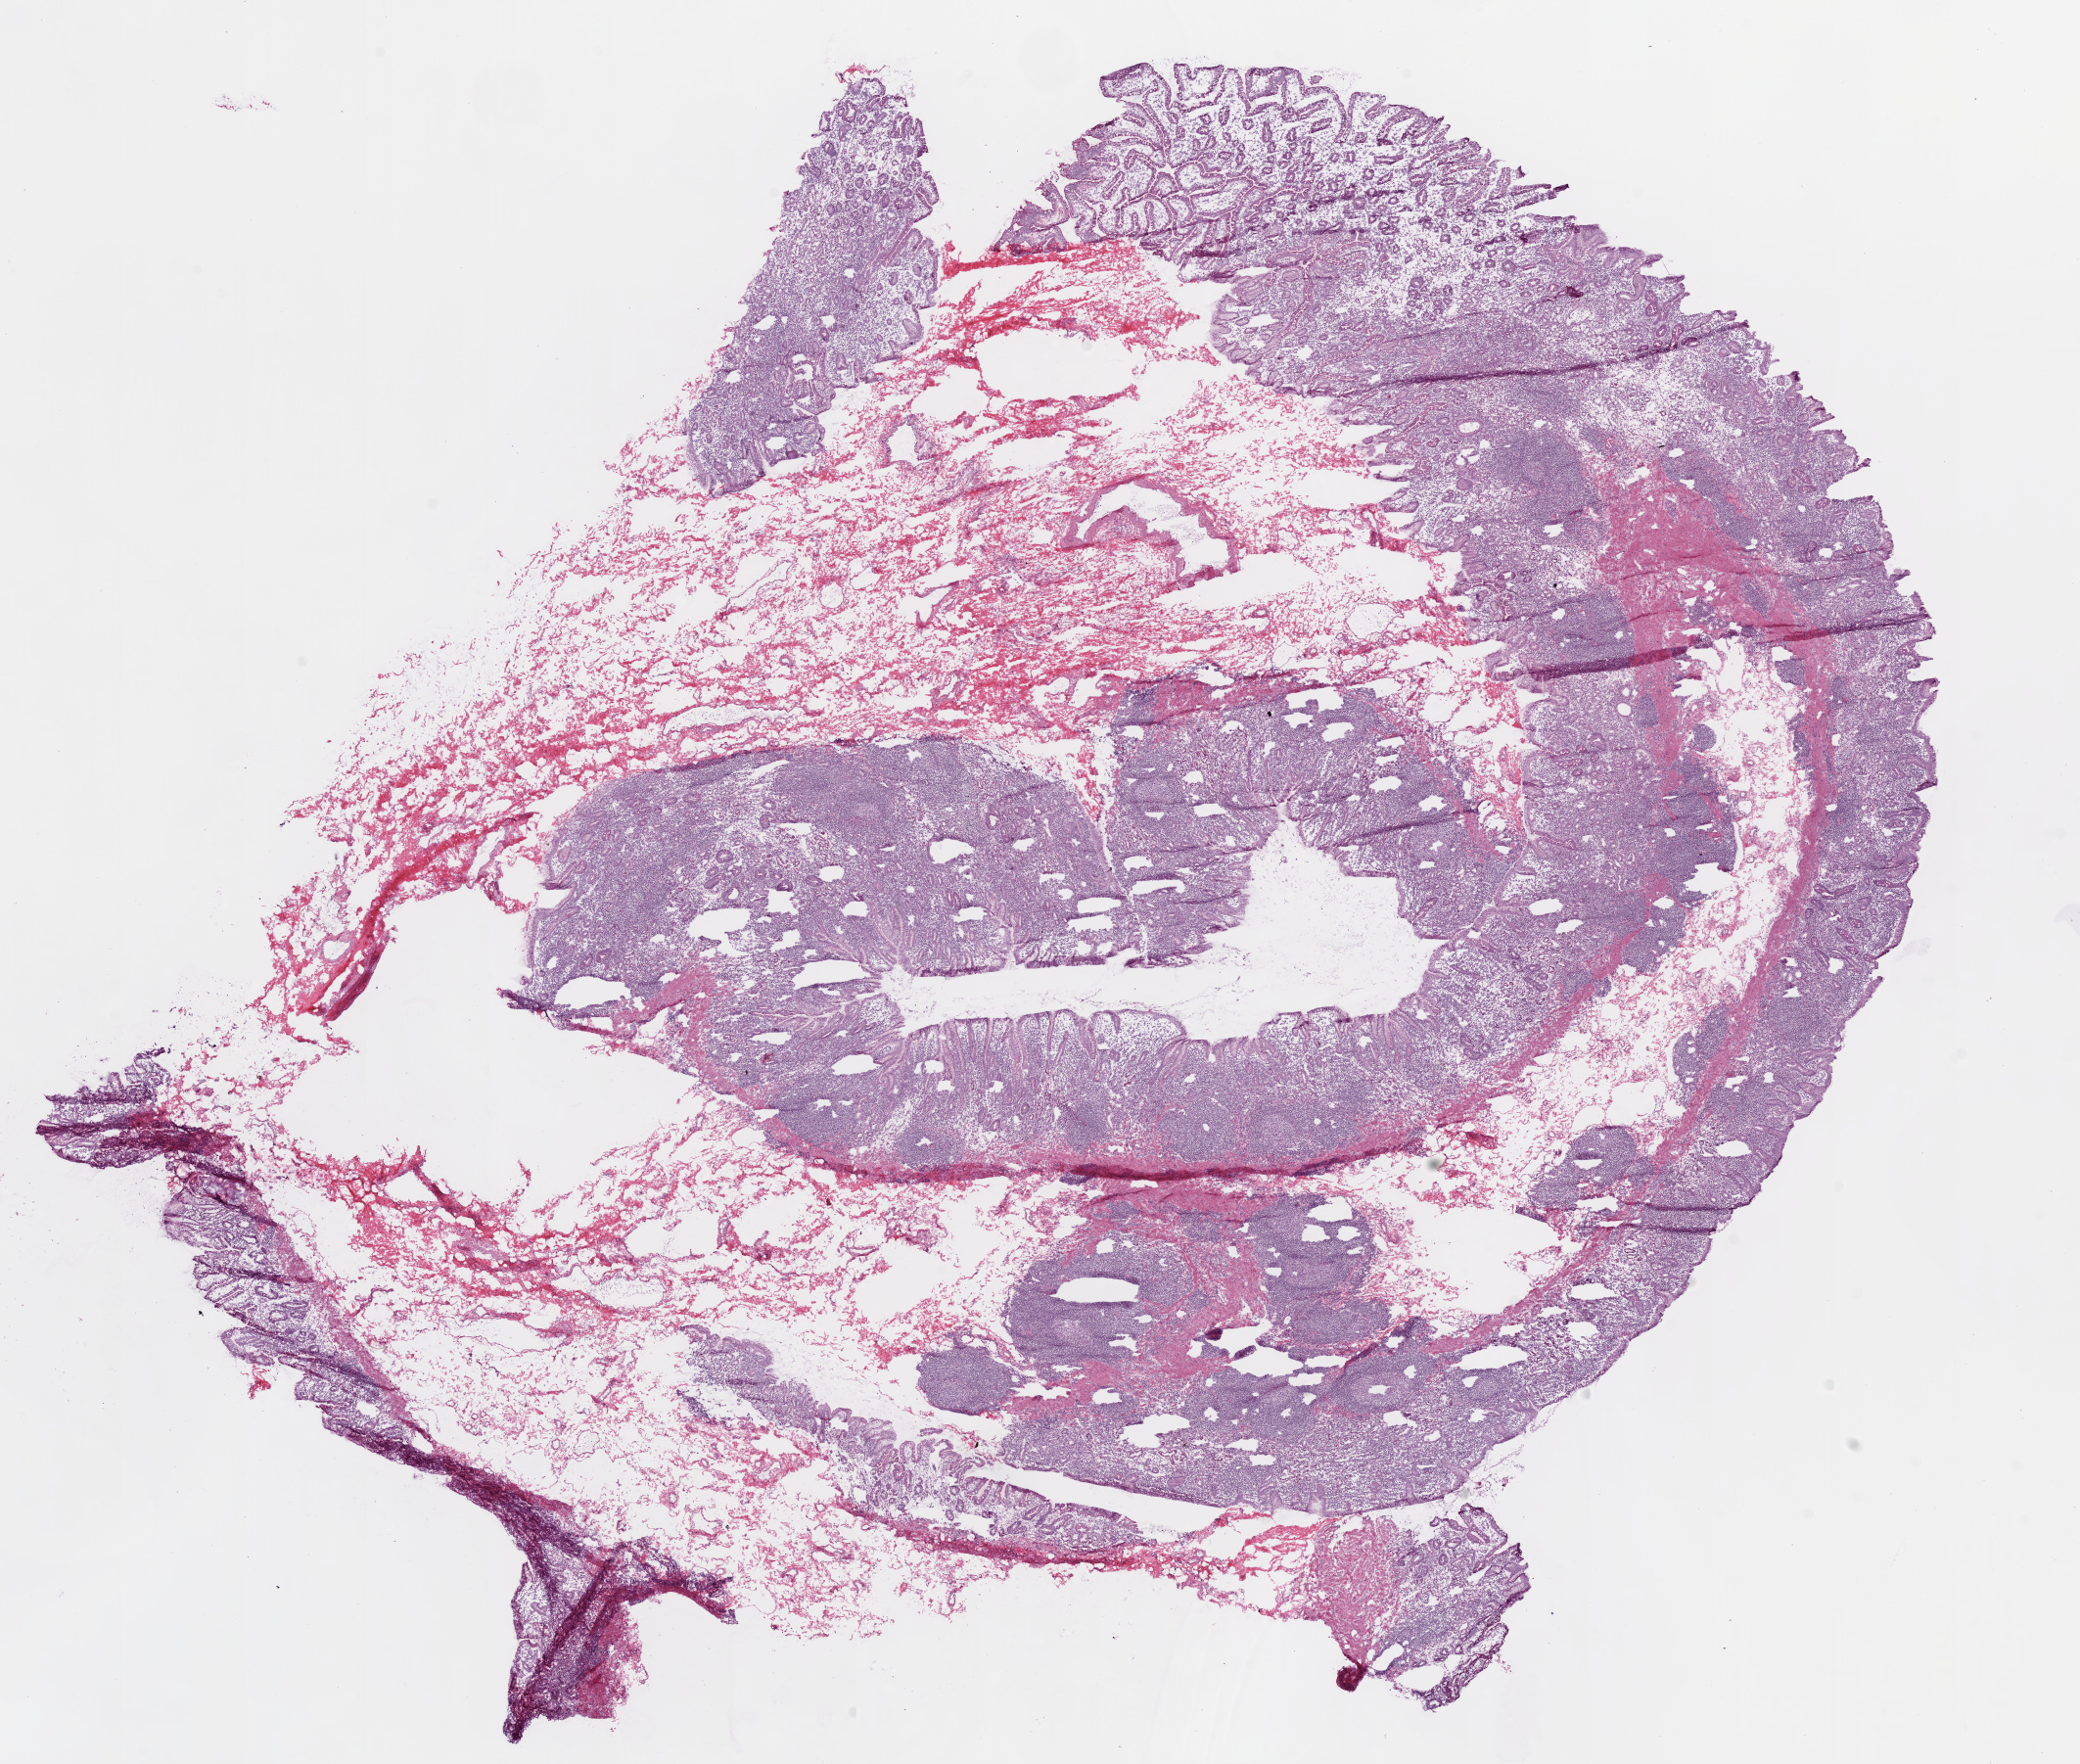
H&E-stained whole-slide image, shown as a low-resolution overview of the whole scanned area (about 17.1 x 14.5 mm); frozen section; stomach, solid tissue normal (non-tumour tissue) sample. Male patient; age at initial diagnosis 70 years.
- this section: solid tissue normal (non-tumour) sample from the same patient
- patient diagnosis: Adenocarcinoma, NOS (gastric antrum)